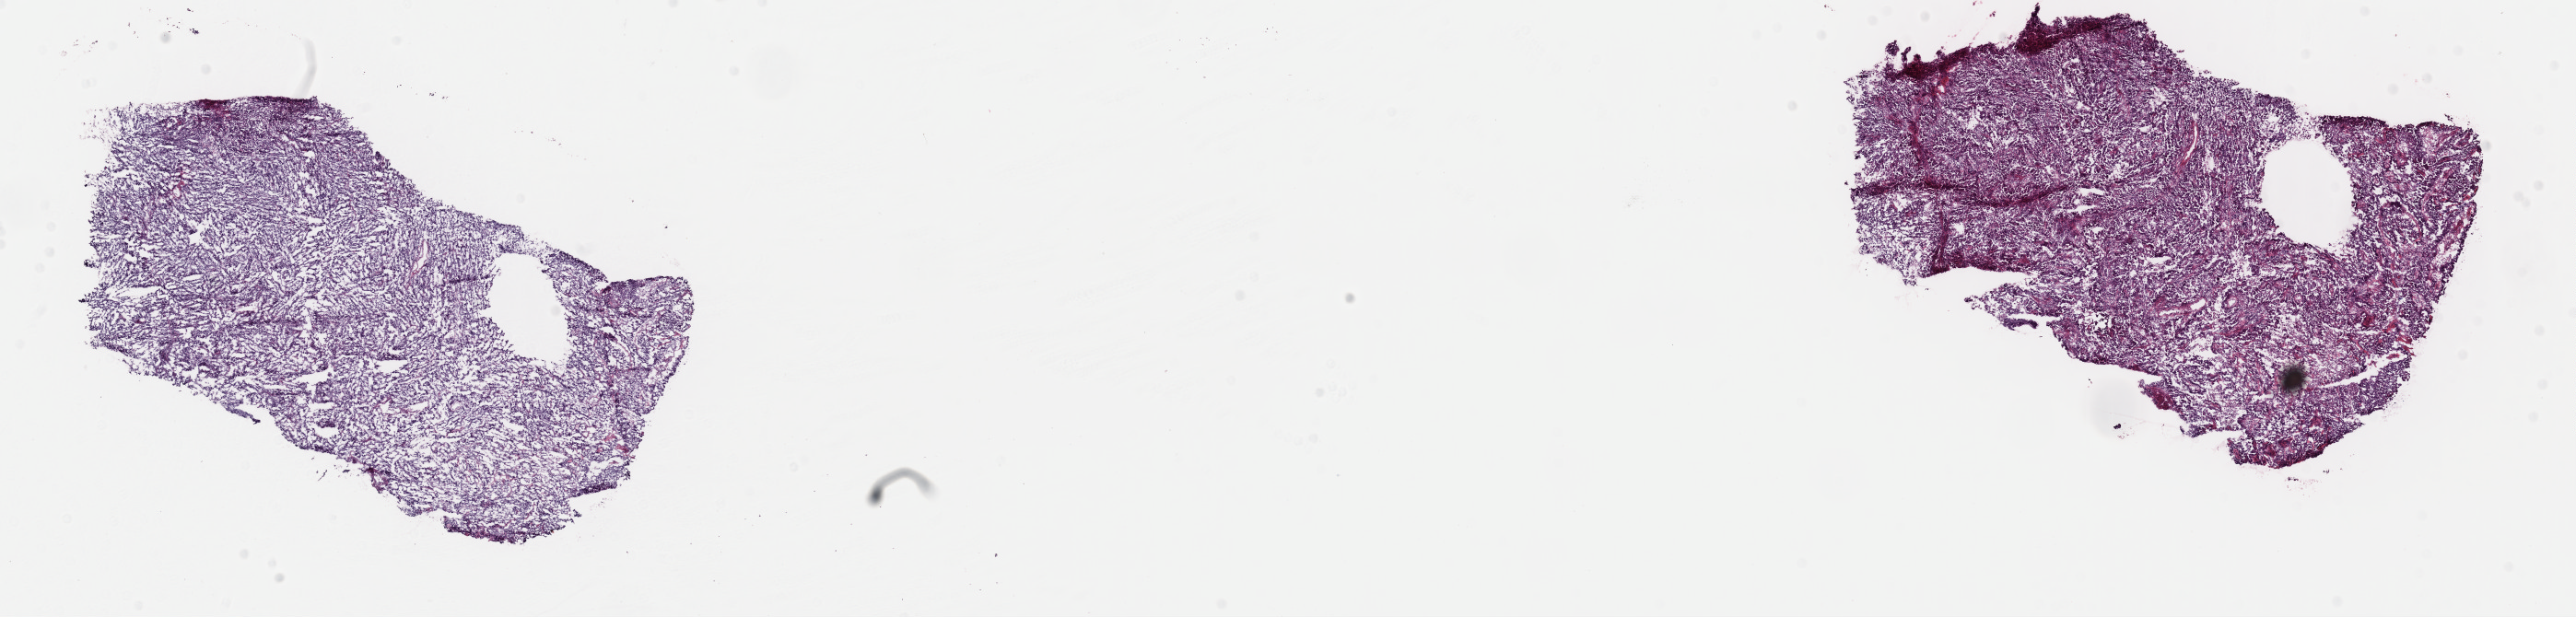
Digitized Hematoxylin and eosin (H&E) stained tissue section (whole slide), shown as a low-resolution overview of the whole scanned area (about 22.1 x 5.3 mm), frozen section from the top of the tissue portion, cervix, primary tumour sample. Female, age 33 years at initial diagnosis. Histologic grade: G3 (poorly differentiated). Pathologist review of this section (percent, as recorded): tumour cells 96%, tumour nuclei 96%, normal cells 0%, stromal cells 2%, necrosis 2%. Inflammatory infiltration, as recorded: lymphocyte infiltration 1%, monocyte infiltration 0%, neutrophil infiltration 0%.
Histologic diagnosis: Adenocarcinoma, endocervical type (cervix uteri). FIGO stage: IB1.